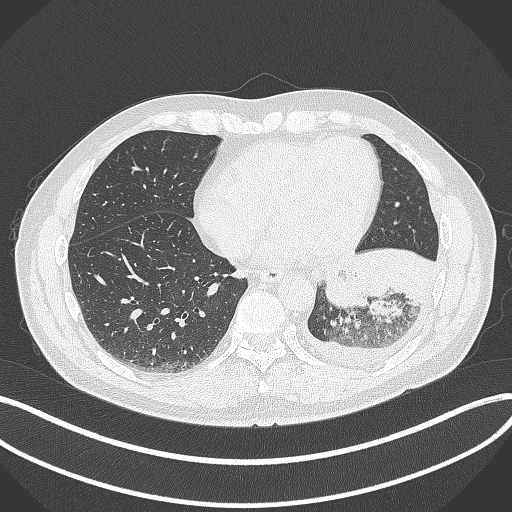
Chest CT, one axial slice. Position 115 of 342 along the scan axis. Reconstruction kernel B70f. 120 kVp. Lung window (W 1500 / L -600 HU). 1 mm slice thickness. 512 × 512 image matrix, field of view 400 × 400 mm. Male patient, age 58 years. Case-level facts recorded for this patient, not image findings: clinical TNM (as recorded): T3 N1 M1b; histopathological grade: G3.
Structures marked on this image (rectangle marked by the reading radiologist):
- lung tumour (recorded histology: small cell carcinoma): bounding box [x1, y1, x2, y2] px = [326, 255, 372, 310]